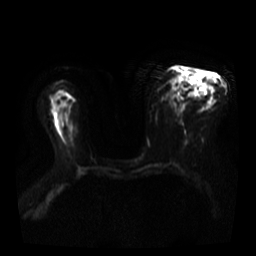
Breast MRI, one axial slice. Slice 19 of 40 in the series (ordered by position). Diffusion-weighted series; image 2 of 4 stored at this slice position (different b-values; order by instance number). 3 T. 5 mm slice thickness. 256 × 256 image matrix. Female patient.
Annotated regions visible in this slice (manually delineated by an expert):
- tumour on diffusion-weighted imaging: bounding box <189,72,204,88> (left, top, right, bottom; pixels)